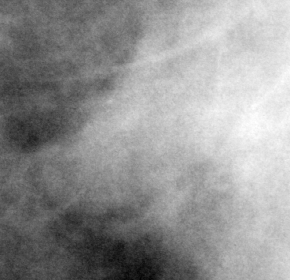
Region of interest cut from a scanned film mammogram (one marked finding); right breast; CC view.
Finding: mass, shape oval, margins ill defined; BI-RADS assessment category 4; subtlety rating 3 on a 1 (subtle) to 5 (obvious) scale; pathology result (as recorded, not read from the image): benign.